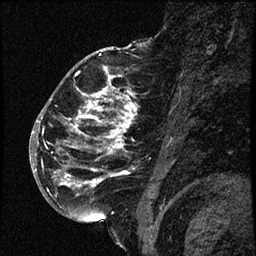
Breast MRI (dynamic contrast-enhanced), one sagittal slice. Slice 37 of 66 in the series (ordered by position). Dynamic contrast-enhanced study with each time point stored as its own series, time point 2 of 3 at this slice position (early post-contrast, ordered by acquisition time). 1.5 T. TE 4.2 ms, TR 17.6 ms. 256 × 256 image matrix, field of view 200 × 200 mm. Female patient. From the clinical record (not read from this slice): setting: breast cancer imaged before/during neoadjuvant chemotherapy; receptor status: HER2-positive.
Structures marked on this image (semi-automatic segmentation, software-assisted and operator-edited):
- analysis volume of interest (the breast-tissue region the enhancement analysis was run in; not a lesion): box from (x=52, y=69) to (x=148, y=209) px
- tumour enhancement mask (voxels above the 100 % enhancement threshold inside the analysis volume of interest): (x=55, y=76)–(x=137, y=188)